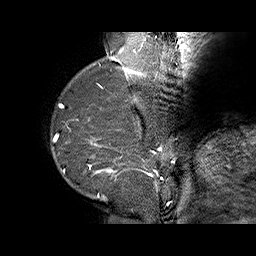
Breast MRI (dynamic contrast-enhanced), one sagittal slice; slice 11 of 70 in the series (ordered by position); dynamic contrast-enhanced series, time point 2 of 6 at this slice position (early post-contrast); 1.5 T; TE 4.5 ms, TR 32.4 ms; 256 × 256 image matrix. Female patient. Case-level facts recorded for this patient, not image findings: setting: breast cancer imaged before/during neoadjuvant chemotherapy; receptor status: HR-positive, HER2-negative.
Annotated regions visible in this slice (semi-automatically segmented with operator editing):
- analysis volume of interest (the breast-tissue region the enhancement analysis was run in; not a lesion): bounding box <71,128,159,202> (left, top, right, bottom; pixels)
- tumour enhancement mask (voxels above the 100 % enhancement threshold inside the analysis volume of interest): <89,137,158,197>